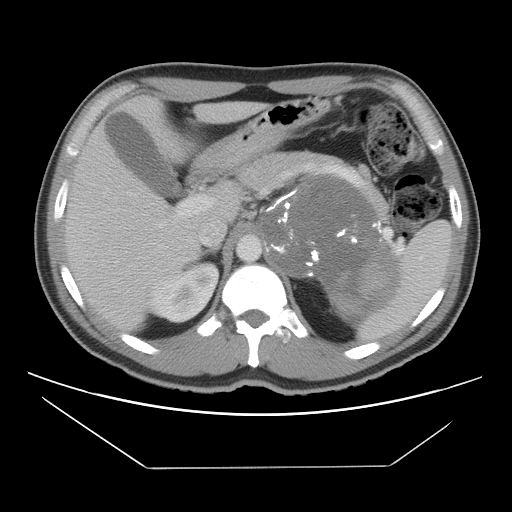
Contrast-enhanced abdominal CT, one axial slice; position 73 of 131 along the scan axis; reconstruction kernel STANDARD; 120 kVp; intravenous contrast given; soft-tissue window (W 400 / L 40 HU); 5 mm slice thickness; 512 × 512 image matrix. Male patient, age 44 years. Case-level facts recorded for this patient, not image findings: diagnosis: adrenocortical carcinoma; tumour side: left adrenal; tumour size at pathology: 15.5 cm; Ki-67 index: 6 %; stage (as recorded): 2.
Annotated regions visible in this slice (semi-automatically segmented with operator editing):
- mass: bounding box [x1, y1, x2, y2] px = [263, 177, 395, 325]